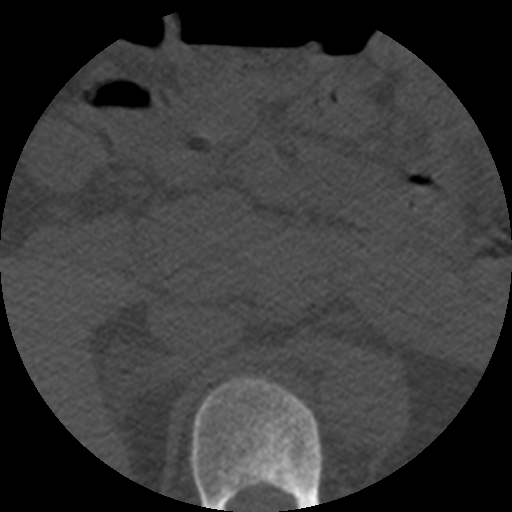
CT including the spine, one axial slice; slice 238 of 508 in the series (ordered by position); bone window (W 1800 / L 400 HU); 1.25 mm slice thickness; 512 × 512 image matrix. Patient age 57 years. Case-level facts recorded for this patient, not image findings: primary cancer: prostate.
Structures marked on this image (semi-automatically segmented with operator editing):
- T11 vertebra: bounding box (x1, y1, x2, y2) in pixels: (191, 377, 323, 512)